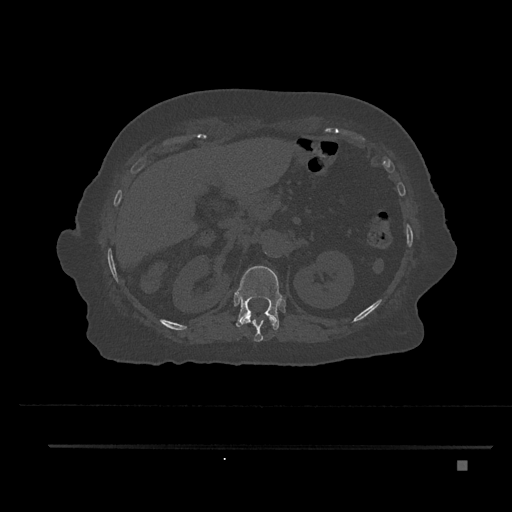
CT including the spine, one axial slice; slice 280 of 797 in the series (ordered by position); reconstruction kernel Br40s/3; 120 kVp; bone window (W 1800 / L 400 HU); 0.5 mm slice thickness; 512 × 512 image matrix, field of view 437 × 437 mm. Patient: female, 76 years. Case-level facts recorded for this patient, not image findings: primary cancer: lung; vertebrae with lytic lesions (as recorded): T11, L3.
Structures marked on this image (semi-automatic segmentation, software-assisted and operator-edited):
- T11 vertebra: bounding box <241,314,275,342> (left, top, right, bottom; pixels)
- T12 vertebra: <236,266,283,330>